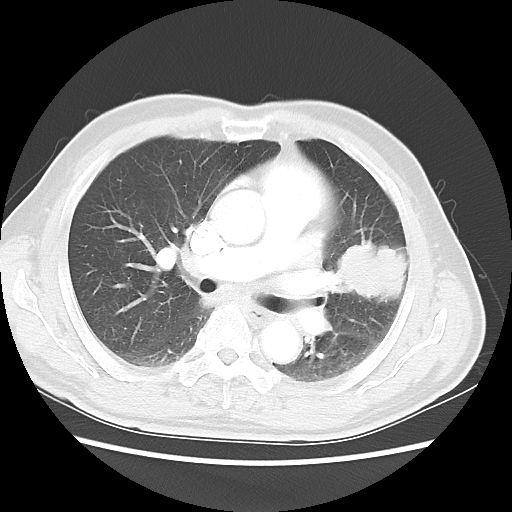
Chest CT, one axial slice; position 29 of 50 along the scan axis; reconstruction kernel LUNG; 120 kVp; lung window (W 1500 / L -600 HU); 5 mm slice thickness; 512 × 512 image matrix, field of view 360 × 360 mm. Patient: male, 69 years. From the clinical record (not read from this slice): clinical TNM (as recorded): T3 N1 M1a.
Outlined on this slice (bounding box drawn by a radiologist):
- lung tumour (recorded histology: squamous cell carcinoma): box from (x=334, y=233) to (x=428, y=327) px